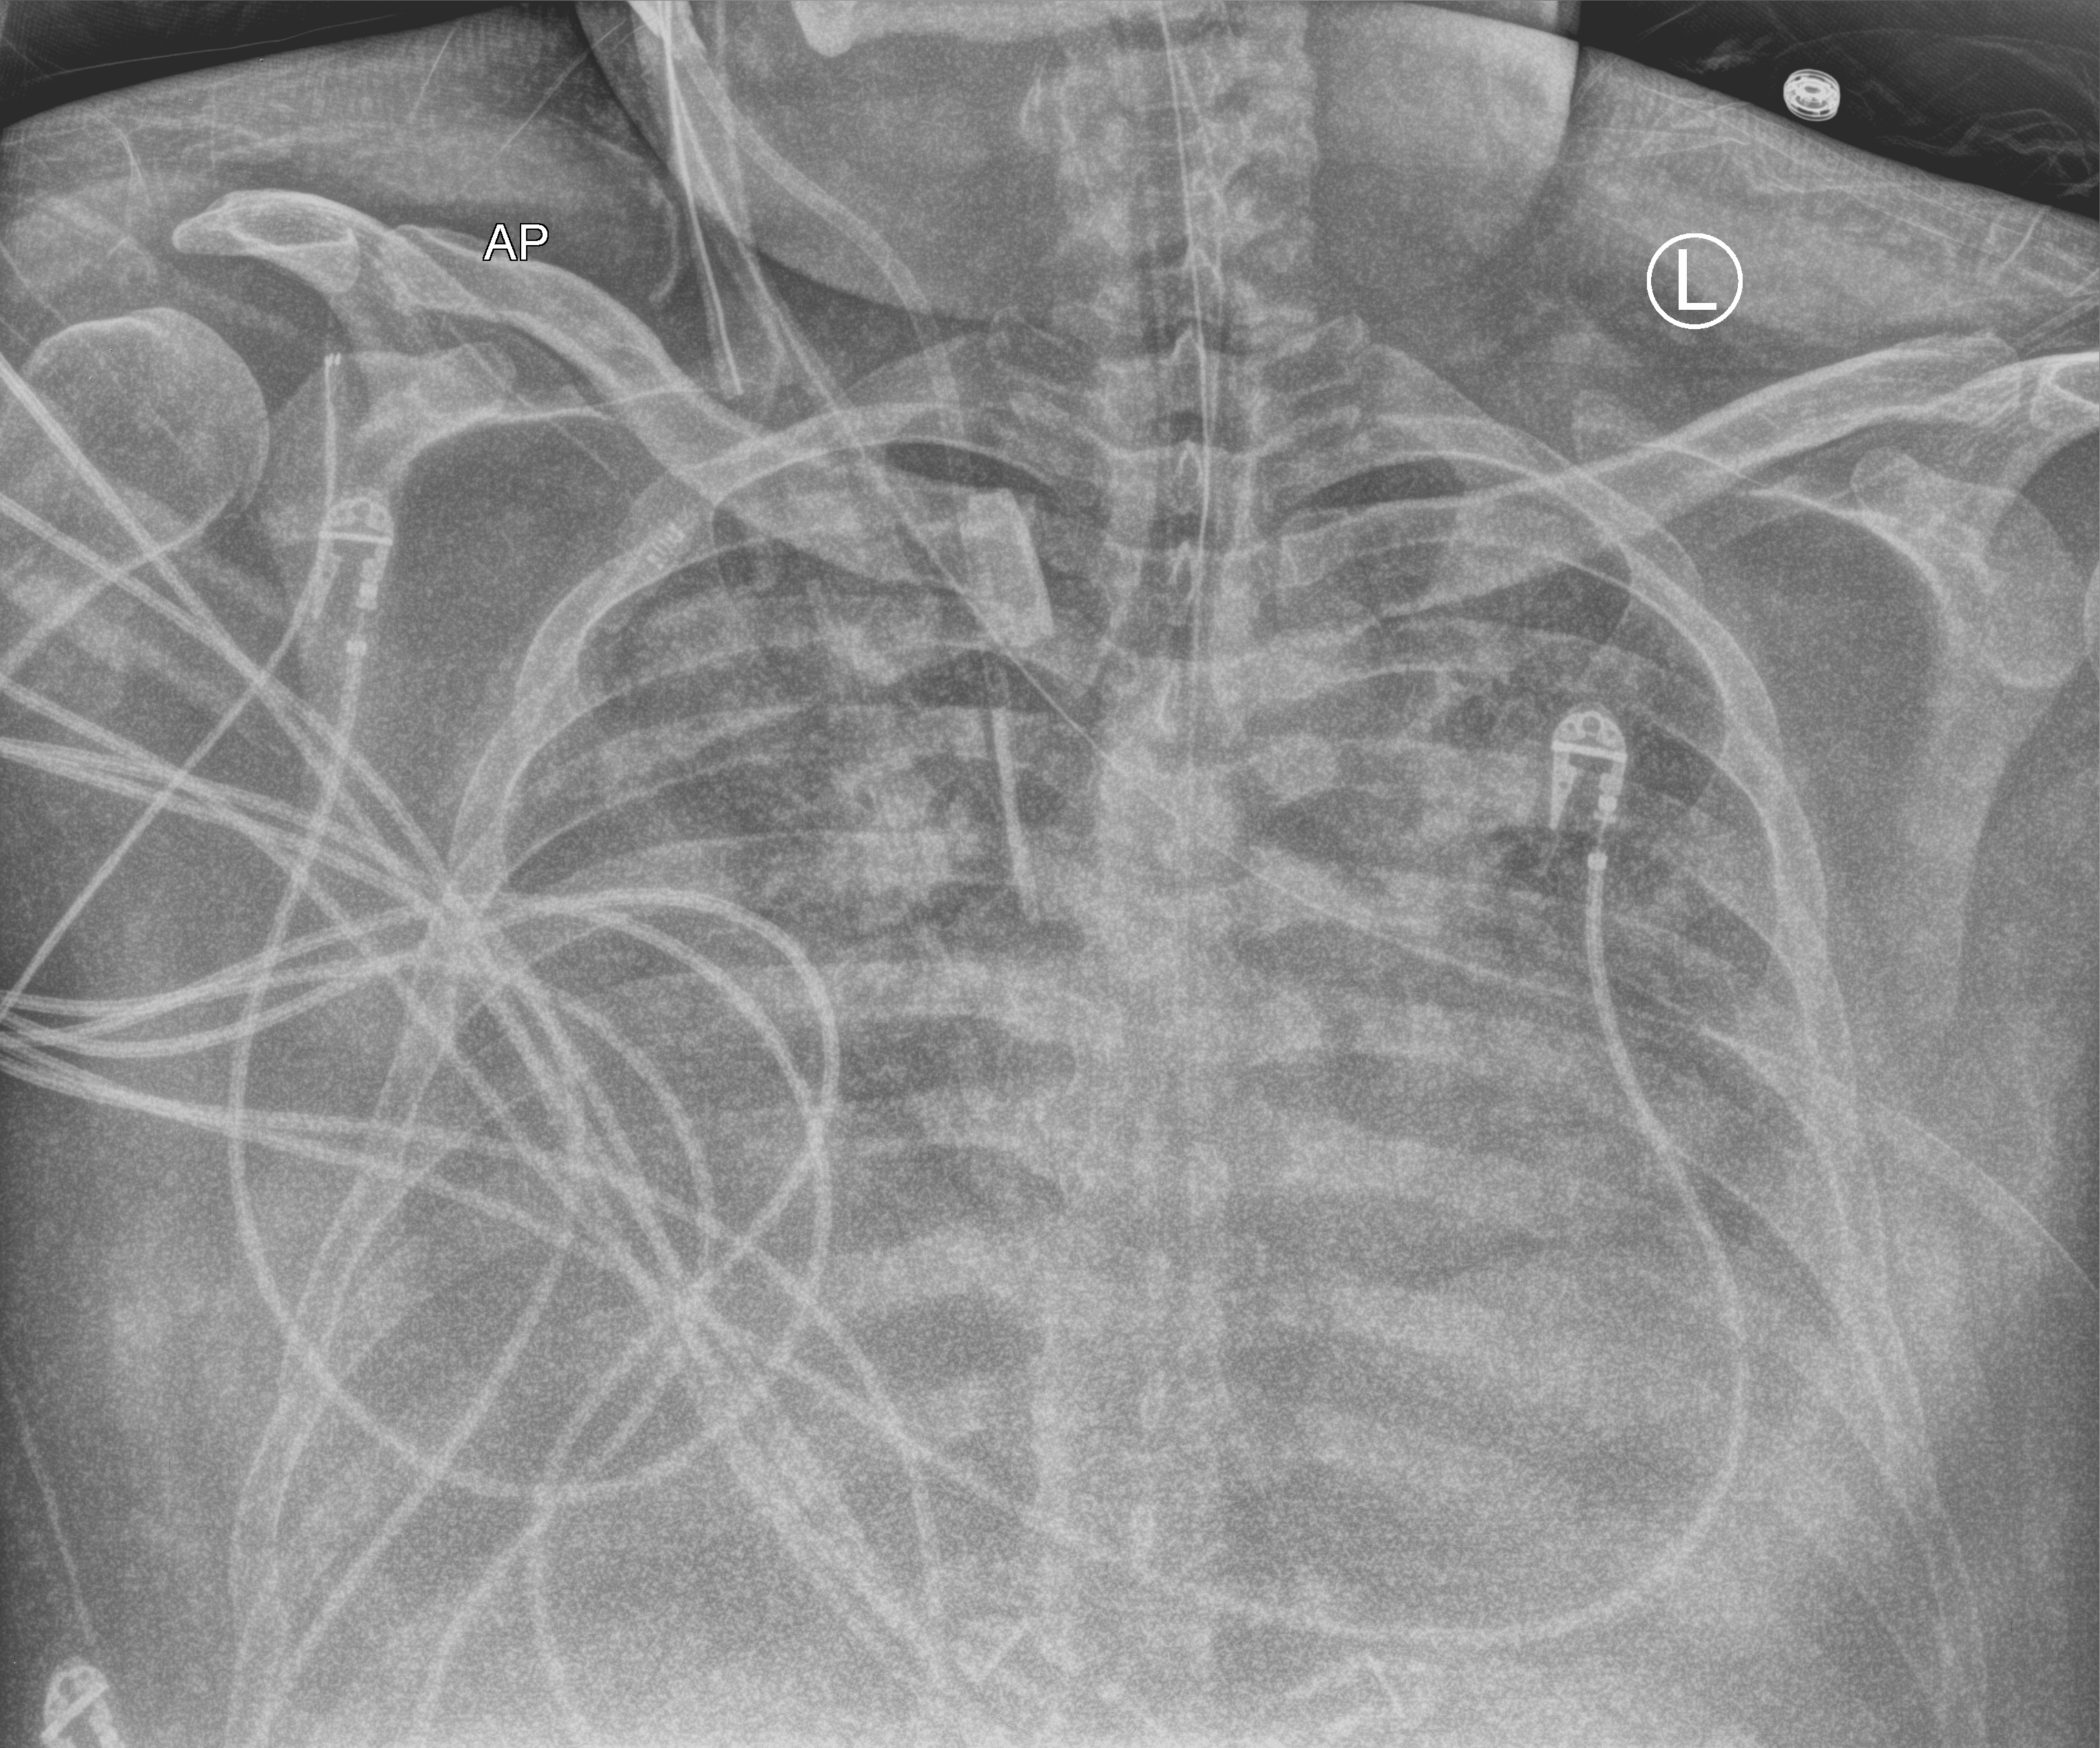
Bedside chest radiograph (computed radiography), anteroposterior (AP) projection. Adult patient hospitalised with COVID-19, age 18–59 years.
From the hospital-stay record, not from the radiograph (when in the stay this image was taken is not recorded):
- length of hospital stay: 22 days
- mechanically ventilated during this hospital stay: yes
- hypertension (admission record): no